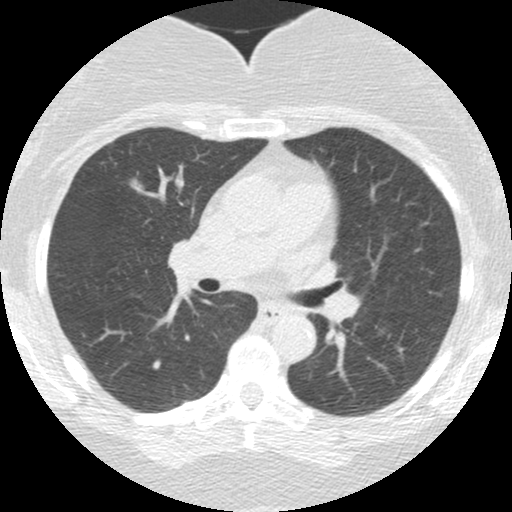
Low-dose screening chest CT, one axial slice; slice 96 of 150 in the series (ordered by position); 120 kVp; lung window (W 1500 / L -600 HU); 2.5 mm slice thickness; 512 × 512 image matrix, field of view 286 × 286 mm.
Structures marked on this image (expert manual segmentation):
- lesion 1 (tumor, upper lobe of right lung): bounding box [x1, y1, x2, y2] px = [129, 178, 143, 192]